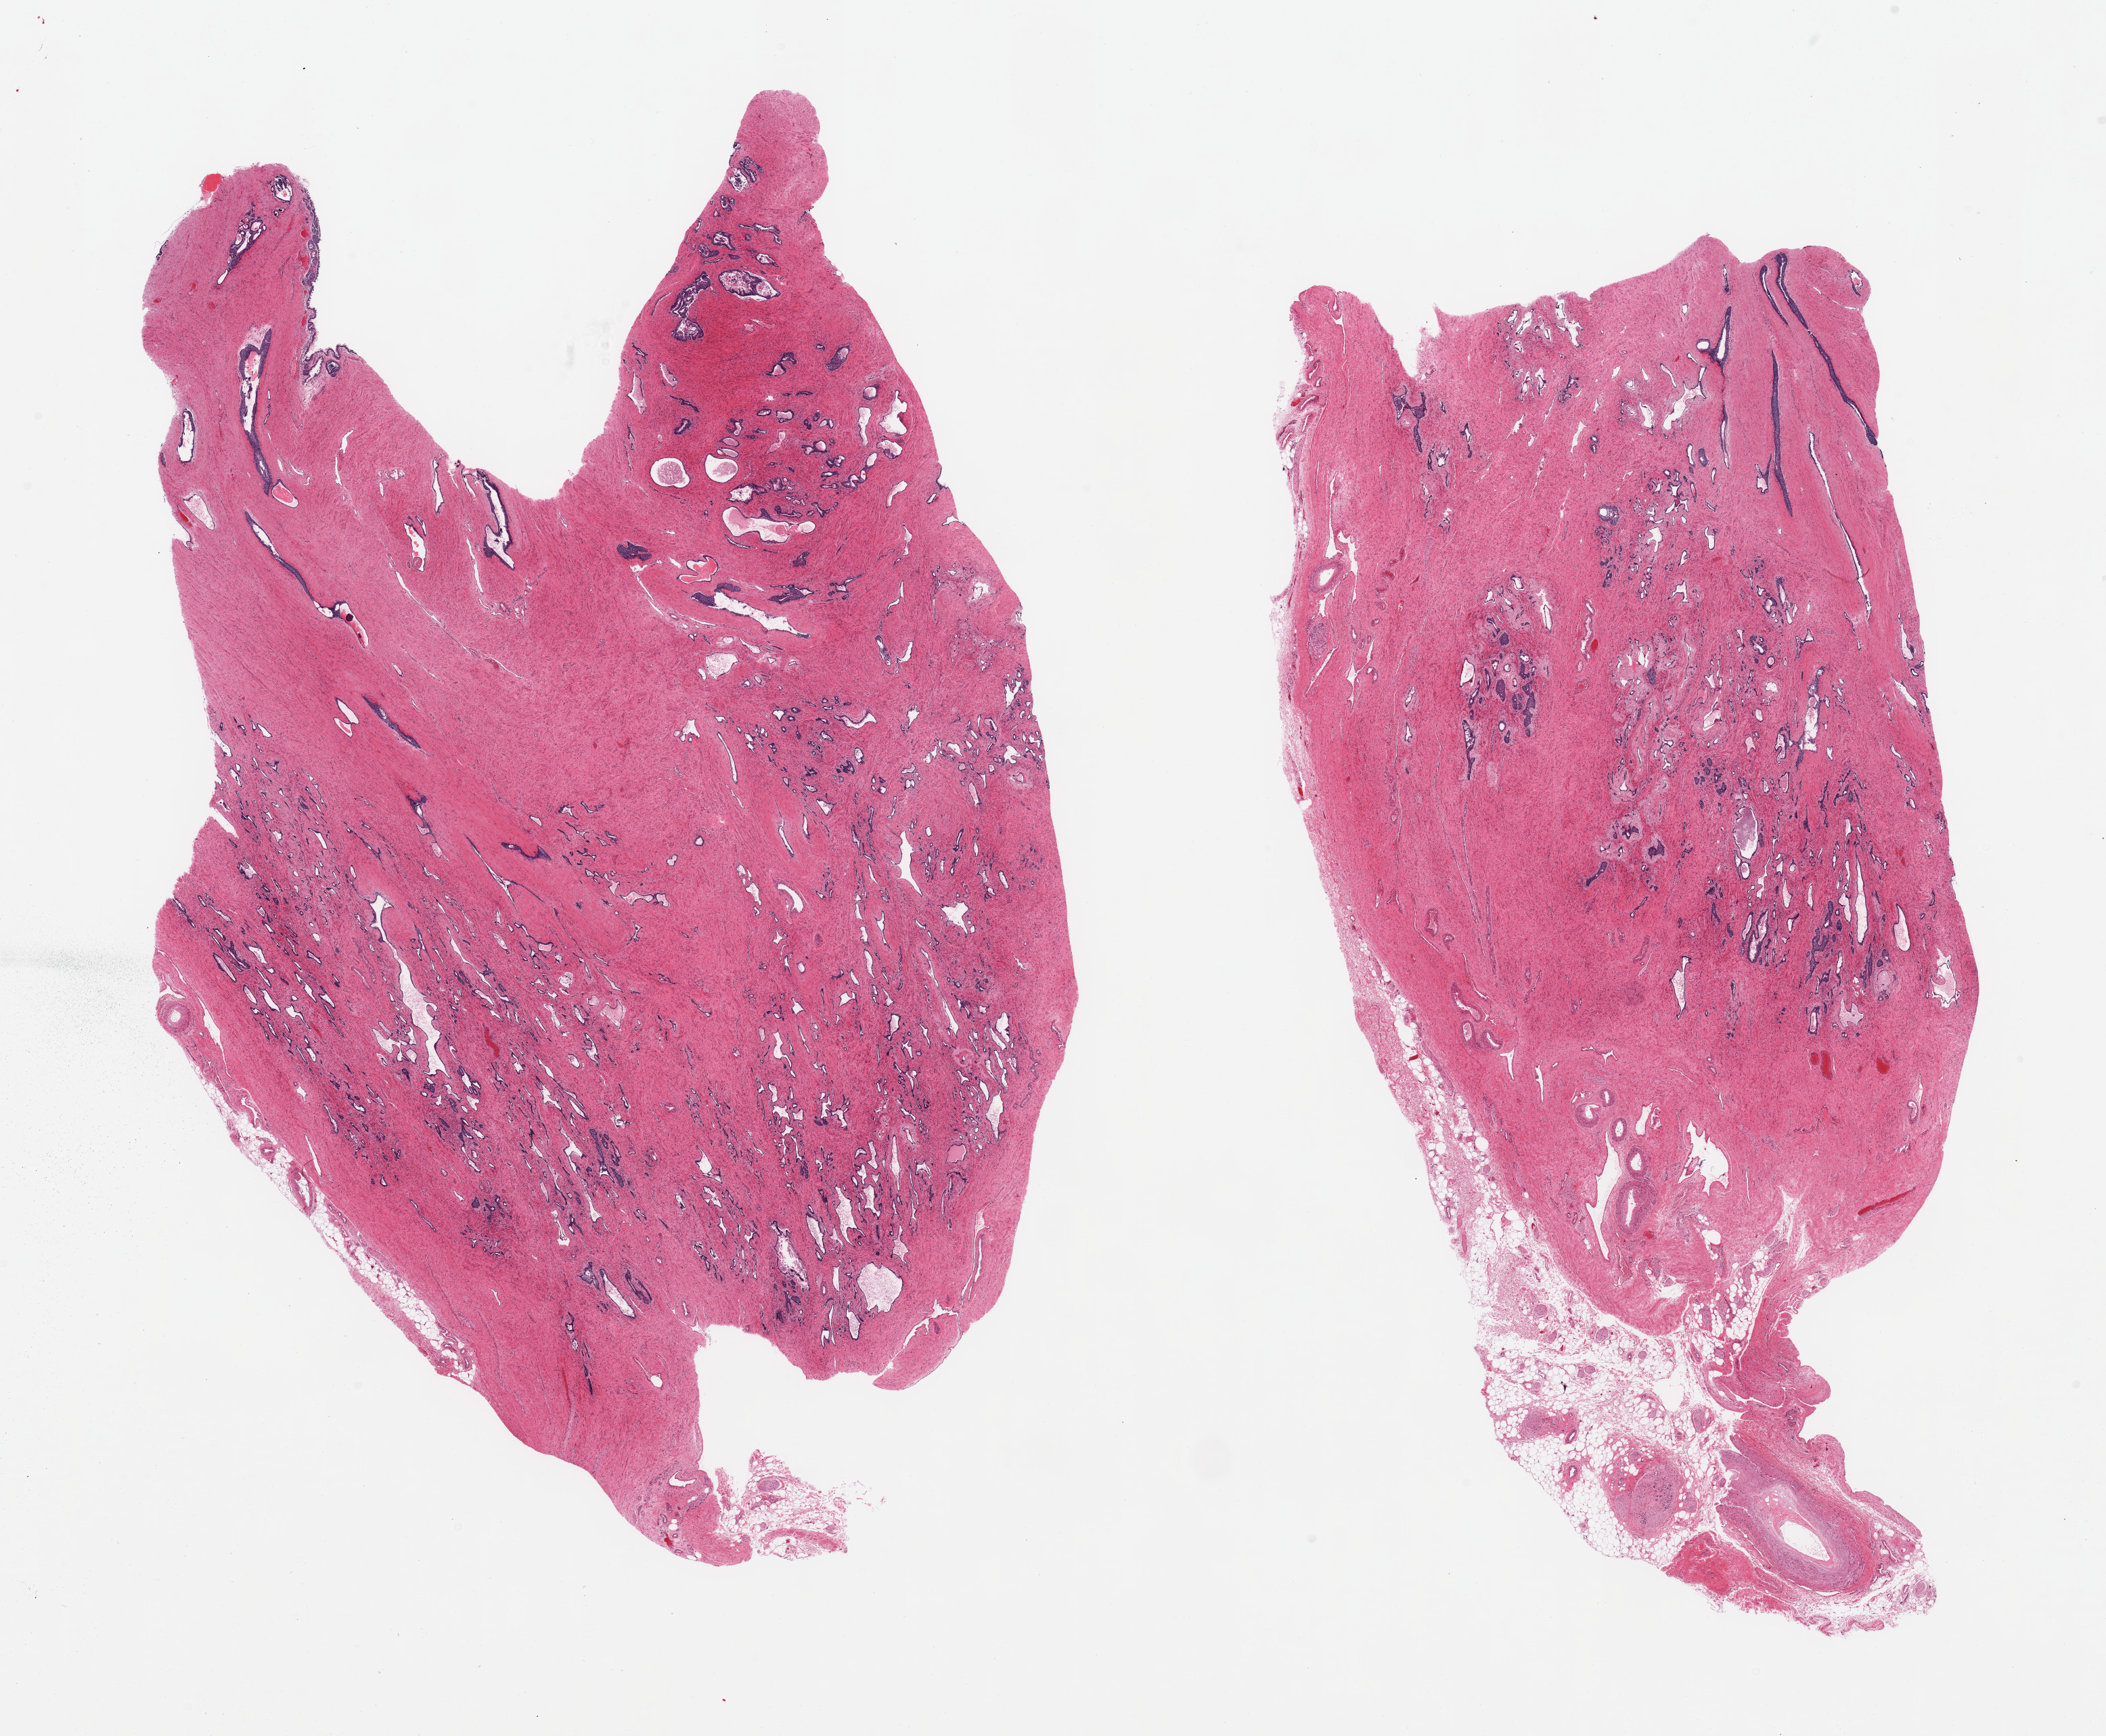
Haematoxylin and eosin whole-slide image, brightfield, low-resolution overview of the scanned area, about 24.6 x 20.3 mm. PAXgene-fixed paraffin-embedded (PFPE) section. Section of prostate (target tissue). Tissue donor sample.
* reviewer comment on this tissue sample: 2 pieces, glandular elements with mild-moderately advanced autolysis